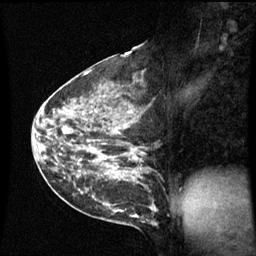
Breast MRI (dynamic contrast-enhanced), one sagittal slice; position 27 of 60 along the scan axis; dynamic contrast-enhanced series, image 2 of 3 at this slice position (ordered by acquisition); 1.5 T; TE 4.2 ms, TR 8.9 ms; 2.4 mm slice thickness; 256 × 256 image matrix, field of view 210 × 210 mm. Patient: female, 42 years. Case-level facts recorded for this patient, not image findings: setting: breast cancer imaged before/during neoadjuvant chemotherapy; receptor status: HER2-positive.
Outlined on this slice (semi-automatically segmented with operator editing):
- analysis volume of interest (the breast-tissue region the enhancement analysis was run in; not a lesion): bounding box <62,93,157,210> (left, top, right, bottom; pixels)
- tumour enhancement mask (voxels above the 70 % enhancement threshold inside the analysis volume of interest): <65,125,135,174>